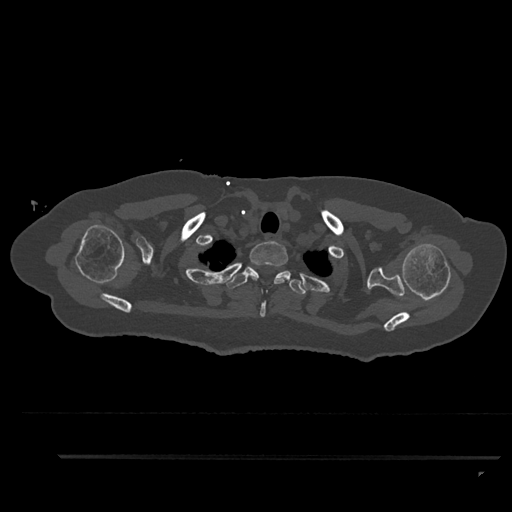
CT including the spine, one axial slice. Position 742 of 797 along the scan axis. Reconstruction kernel Br40s/3. 120 kVp. Bone window (W 1800 / L 400 HU). 0.5 mm slice thickness. 512 × 512 image matrix. Female patient, age 44 years. From the clinical record (not read from this slice): primary cancer: renal; vertebrae with lytic lesions (as recorded): L1.
Outlined on this slice (semi-automatic segmentation, software-assisted and operator-edited):
- T1 vertebra: bounding box [x1, y1, x2, y2] px = [247, 241, 288, 317]
- T2 vertebra: [226, 266, 306, 294]